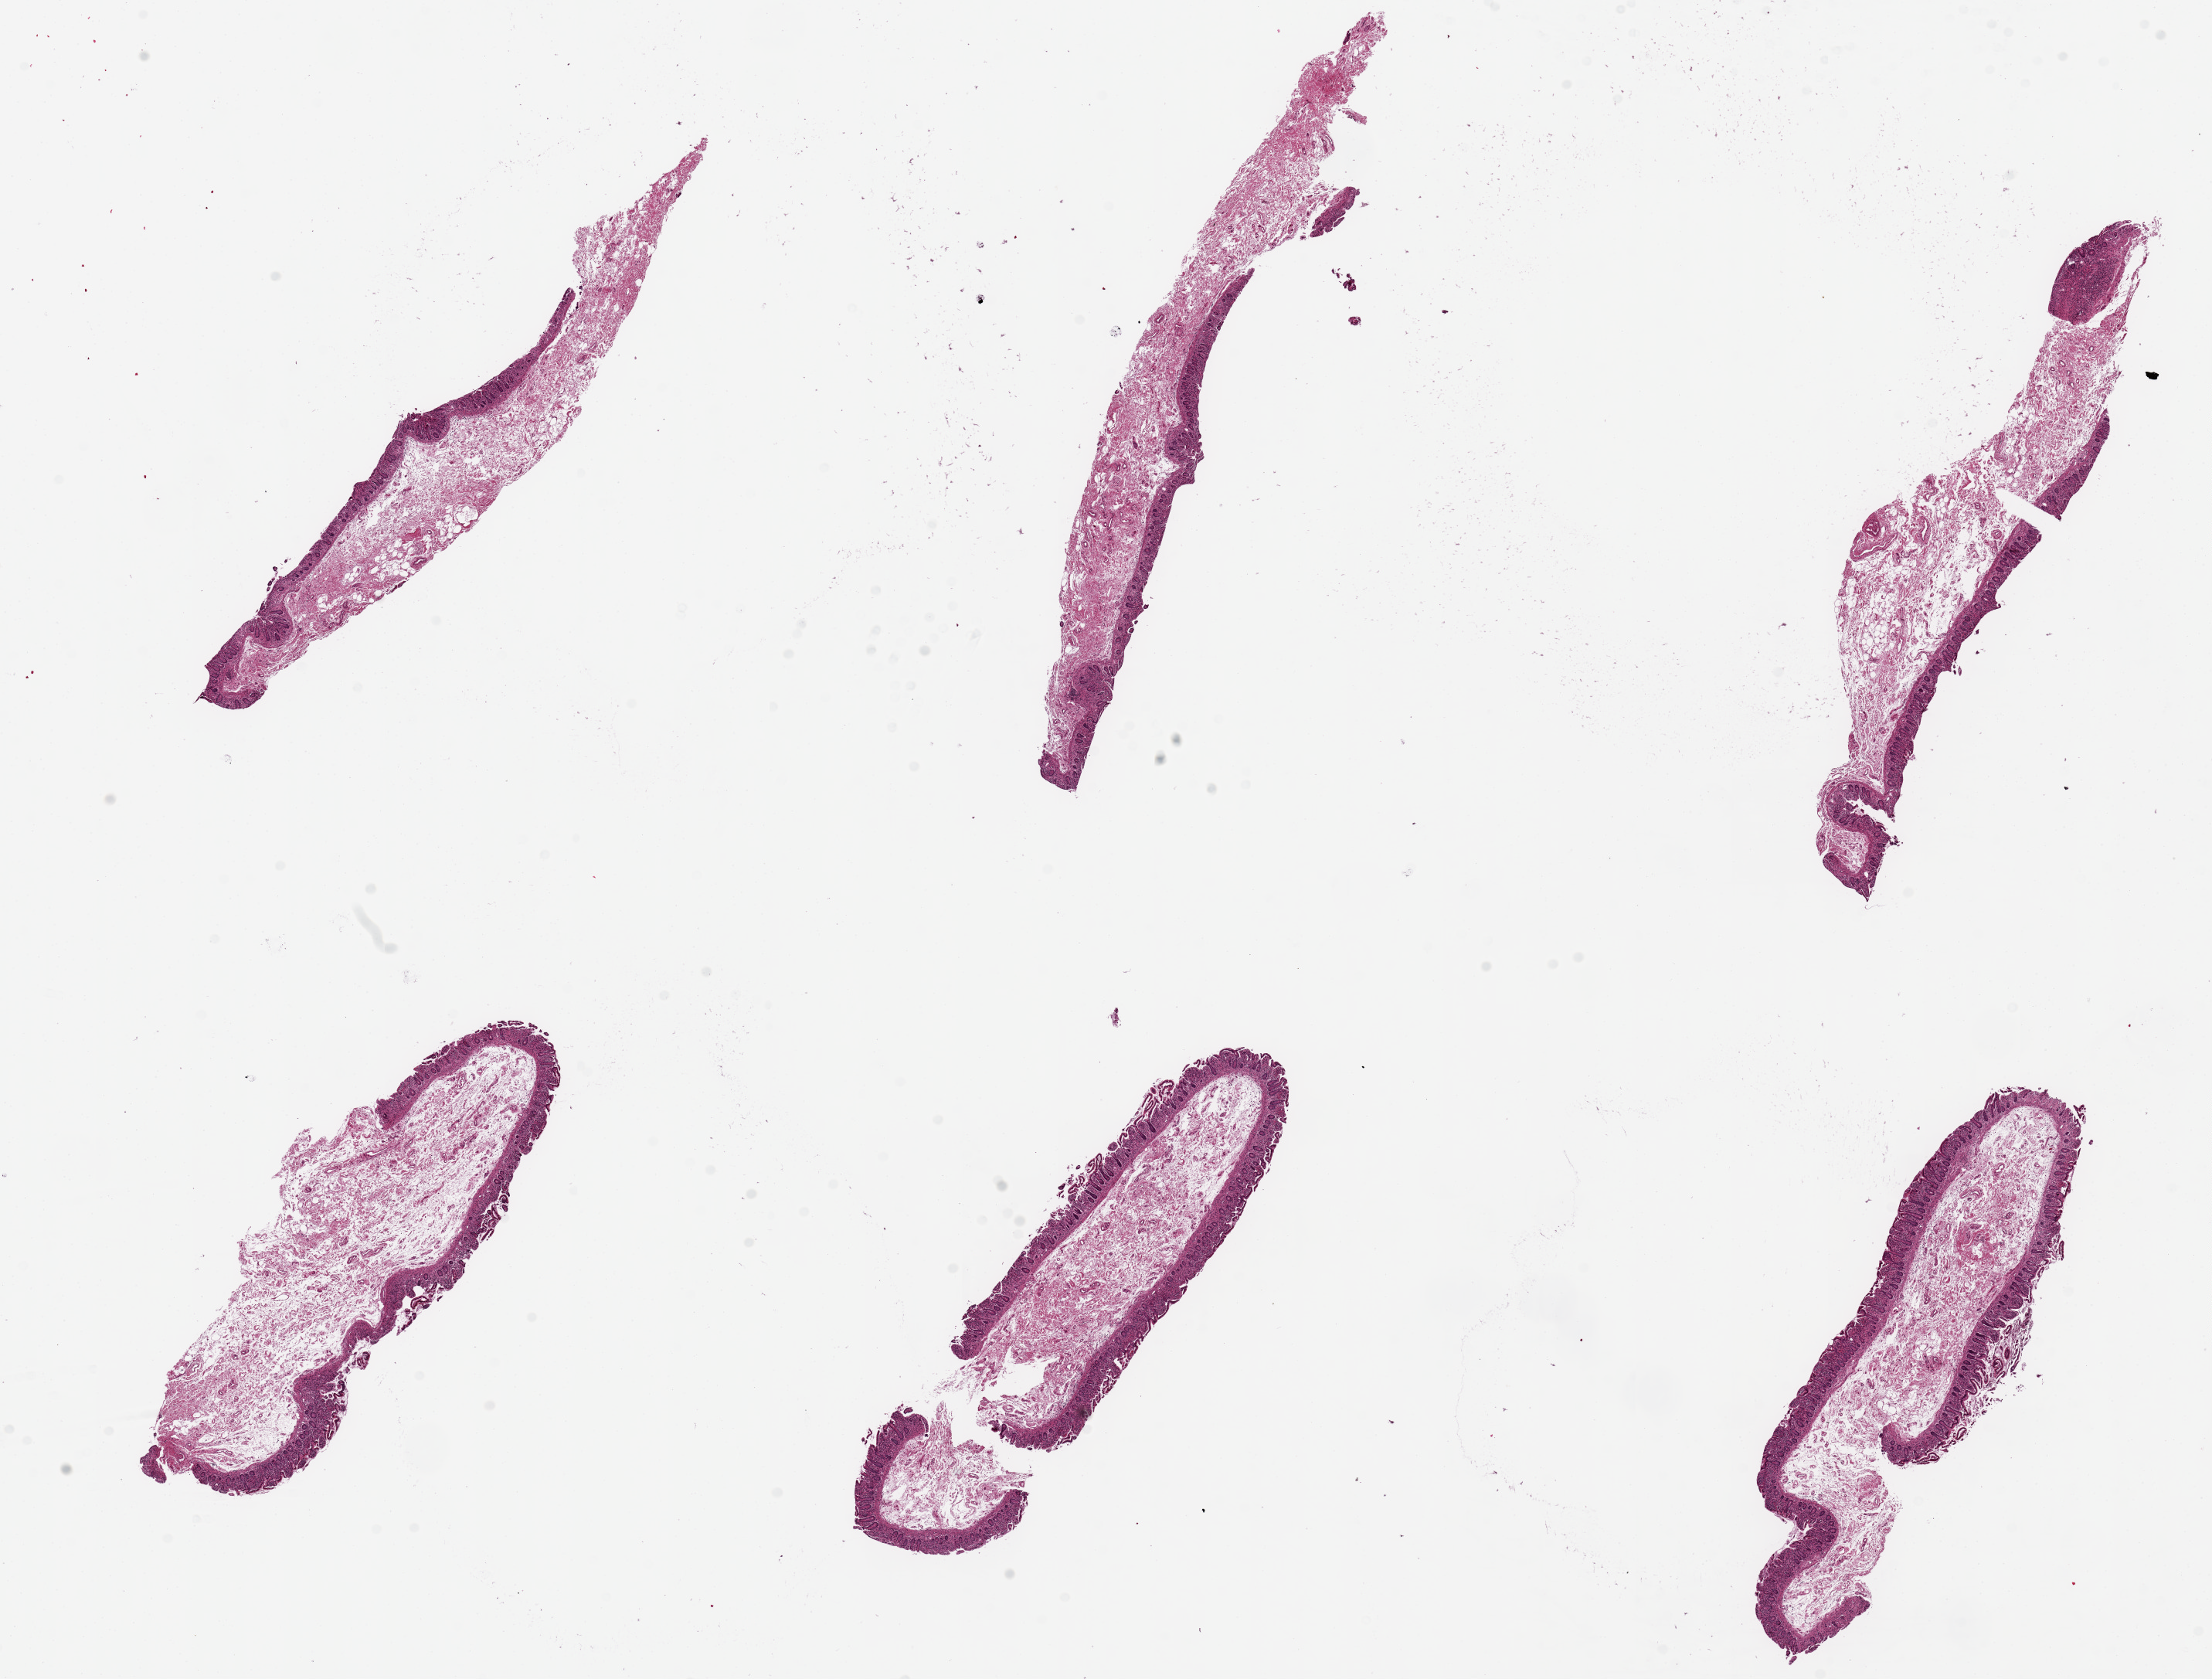
Whole-slide image, hematoxylin and eosin (H&E) stain, shown as a low-resolution overview of the whole scanned area (about 22.6 x 17.2 mm, slide scanned at 20x). PAXgene-fixed paraffin-embedded (PFPE) section. Target tissue: ileum. Tissue donor sample. Female donor.
Pathologist's review note for this sample: 6 pieces, up to 8.5x2mm; mucosa sloughed.